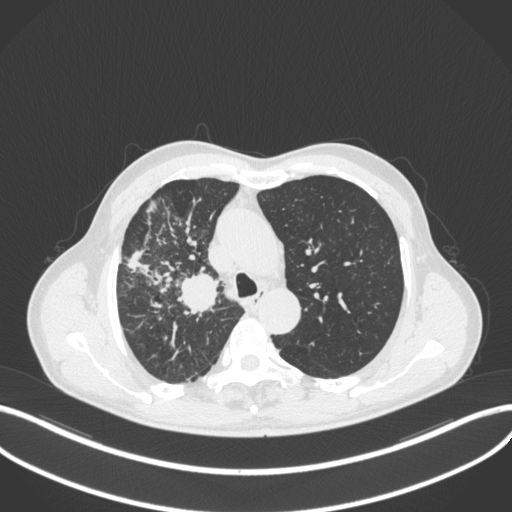
Chest CT, one axial slice; position 344 of 490 along the scan axis; lung window (W 1500 / L -600 HU); 1 mm slice thickness; 512 × 512 image matrix, field of view 400 × 400 mm. Male patient, age 69 years. Case-level facts recorded for this patient, not image findings: clinical TNM (as recorded): T2a N0 M0.
Annotated regions visible in this slice (bounding box drawn by a radiologist):
- lung tumour (recorded histology: adenocarcinoma): bounding box (x1, y1, x2, y2) in pixels: (173, 271, 224, 317)